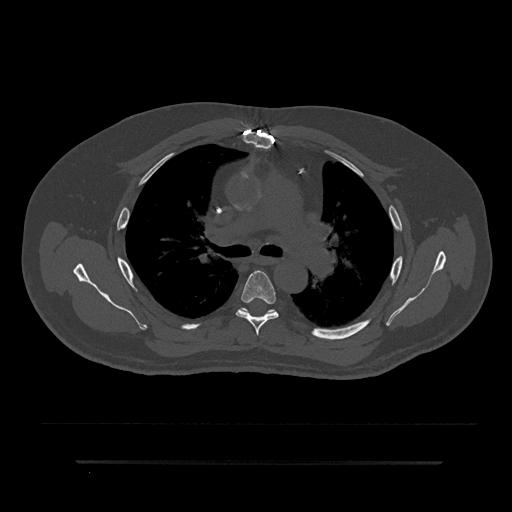
CT including the spine, one axial slice; position 567 of 797 along the scan axis; 120 kVp; bone window (W 1800 / L 400 HU); 512 × 512 image matrix, field of view 464 × 464 mm. Patient: male, 59 years. From the clinical record (not read from this slice): primary cancer: bile ducts.
Outlined on this slice (semi-automatic segmentation, software-assisted and operator-edited):
- T5 vertebra: bounding box (x1, y1, x2, y2) in pixels: (236, 270, 279, 335)
- T6 vertebra: (239, 308, 272, 314)